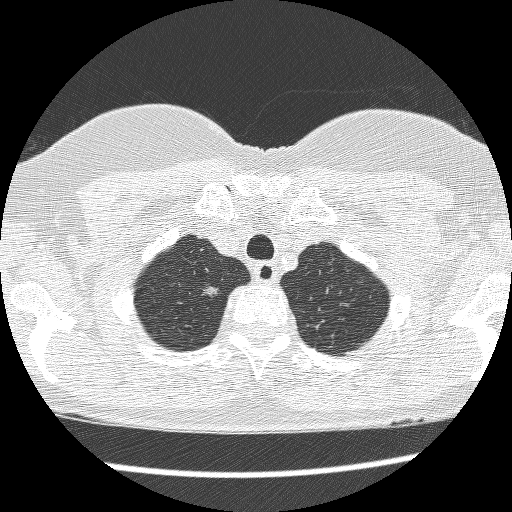
Low-dose screening chest CT, axial slice, first (baseline) screen, lung window (W 1500 / L -600 HU), 1.25 mm slice thickness, lung (sharp) reconstruction kernel (BONE). Female participant, aged 61 years at enrolment. Current smoker at enrolment.
Expert-annotated lung lesion, box from (x=196, y=281) to (x=226, y=305) px. Screening reader's record for this exam (one nodule recorded; not confirmed to be the boxed lesion): non-calcified nodule or mass ≥4 mm, right upper lobe, 7 × 6 mm, poorly defined margins, mixed attenuation. Participant outcome: lung cancer diagnosed 403 days after this screen — adenocarcinoma, NOS, right upper lobe, poorly differentiated (G3), 12 mm at pathology.